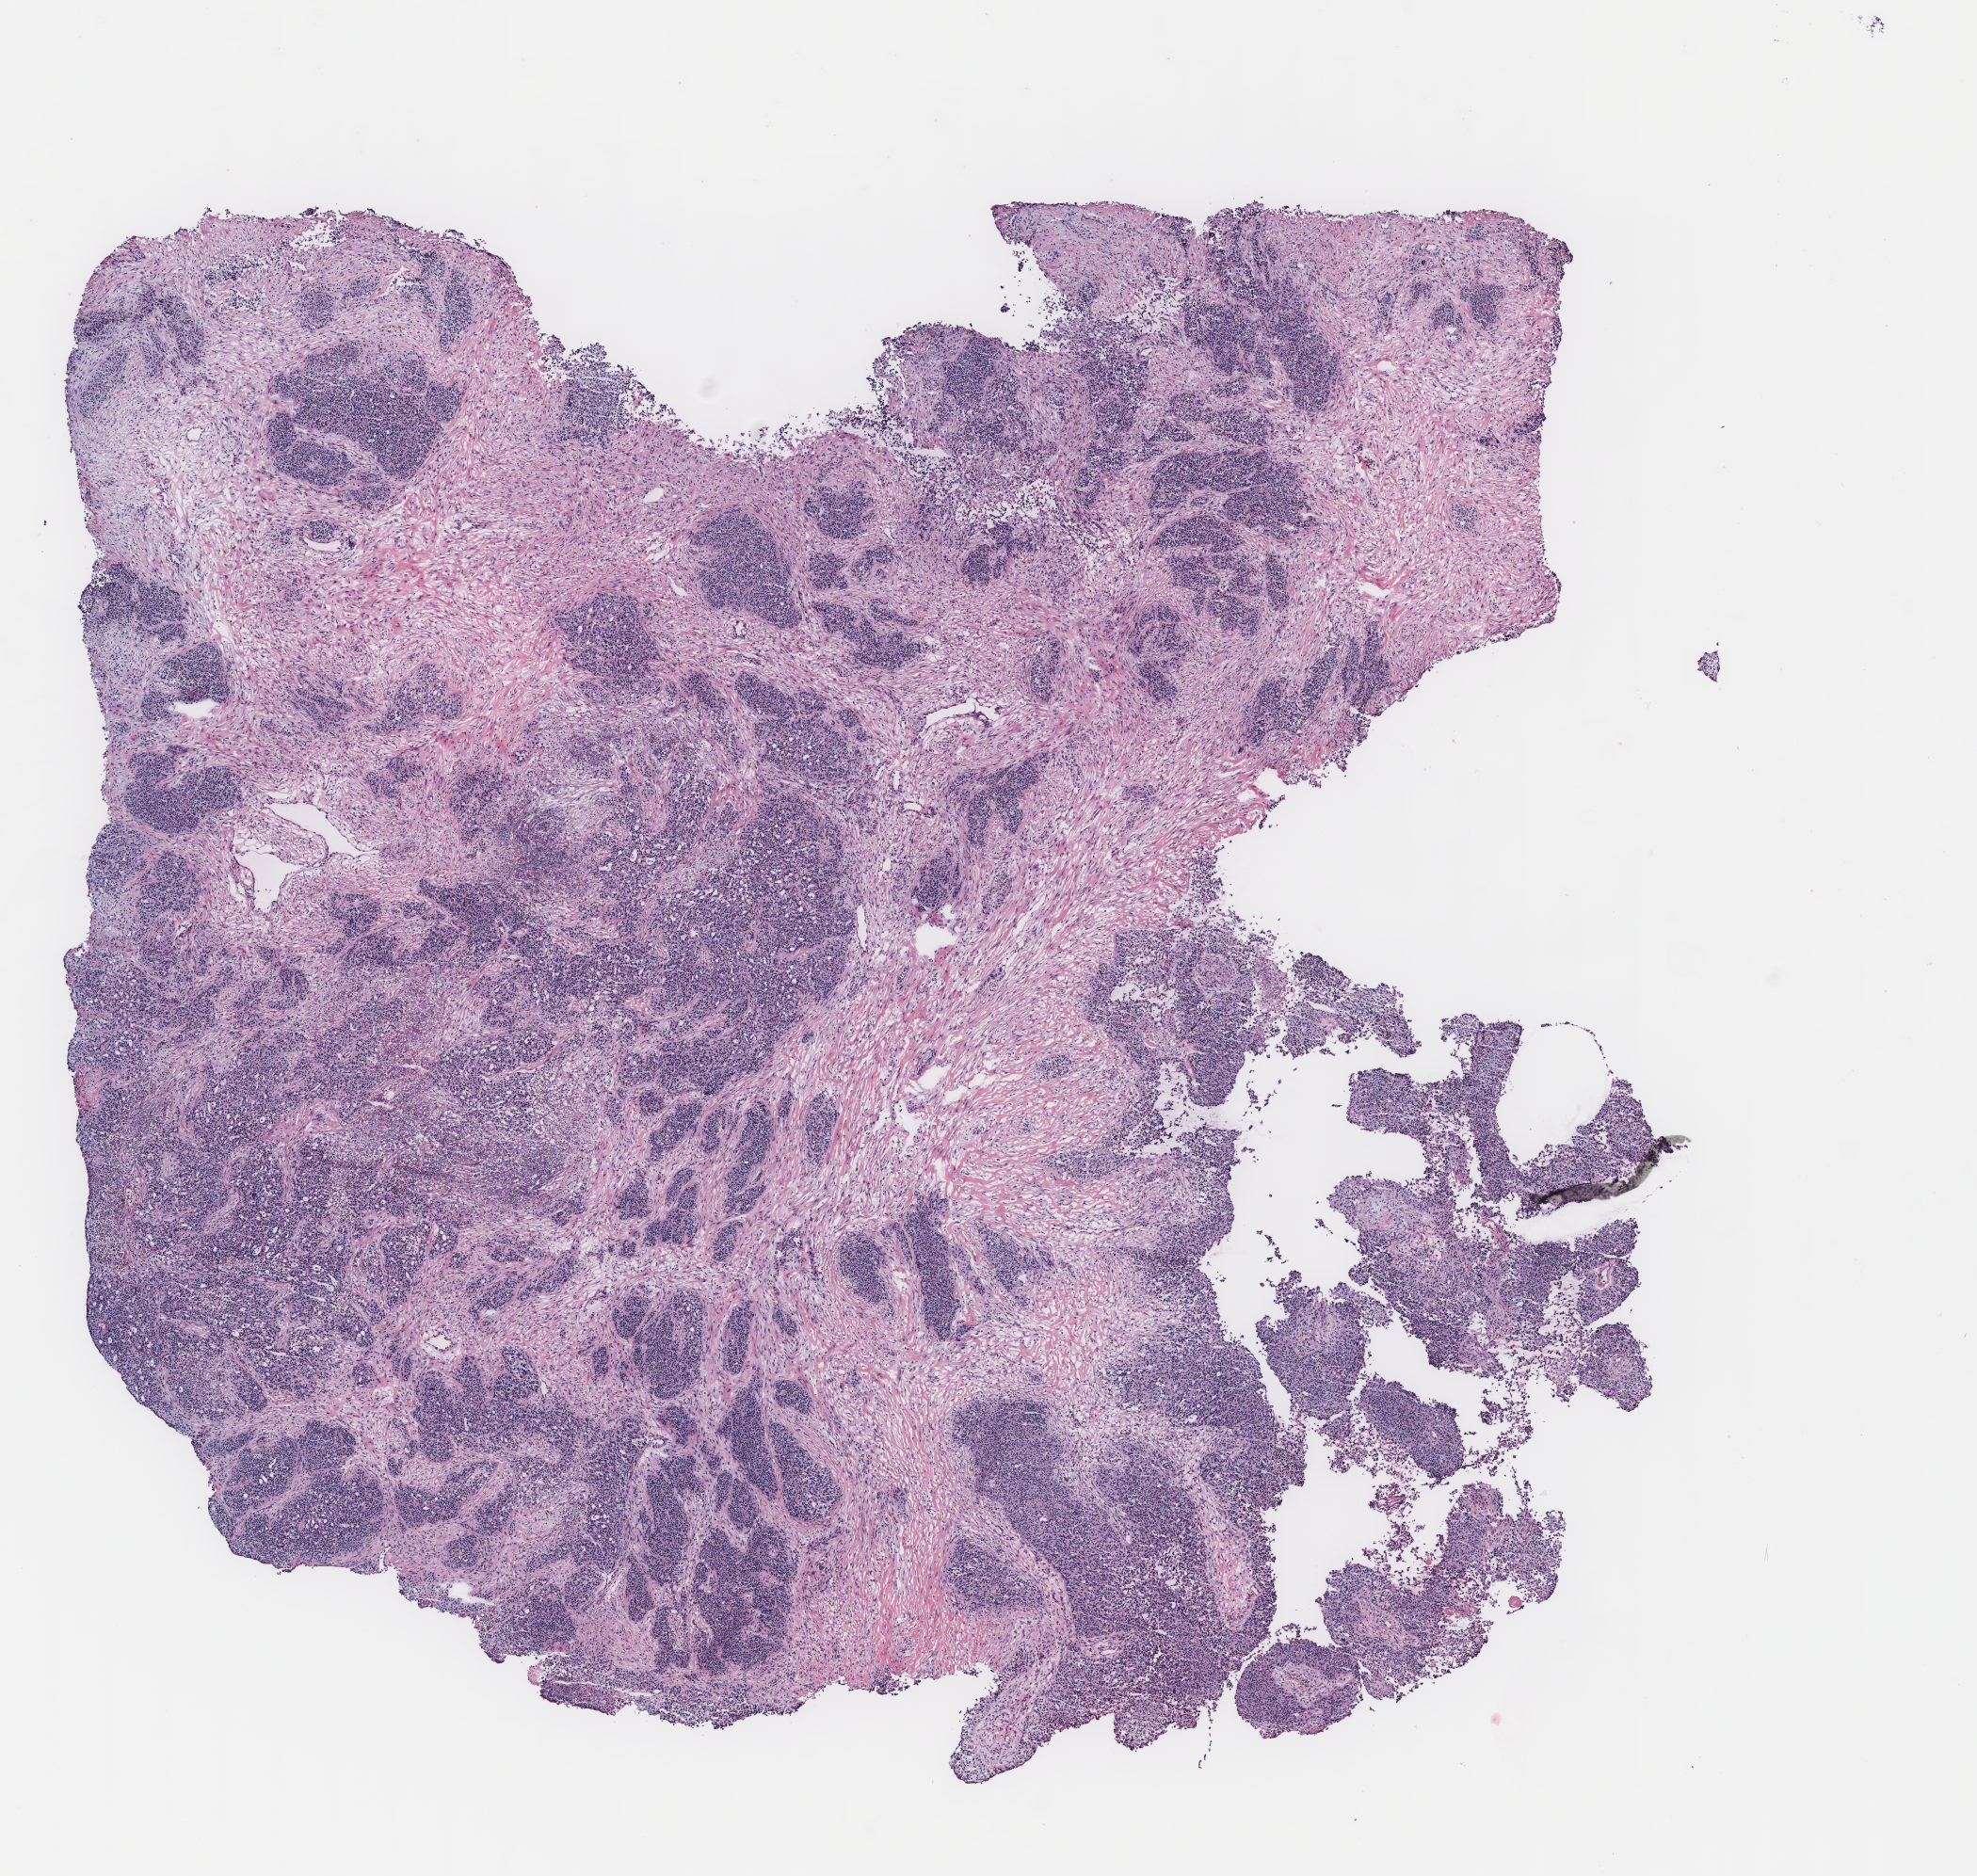
H&E whole-slide image, whole scanned area (about 8.4 x 8.0 mm, acquisition: 40x scan) shown as a low-resolution overview; ovary, tissue type not recorded. Female patient.
Patient diagnosis: Serous adenocarcinoma, NOS.